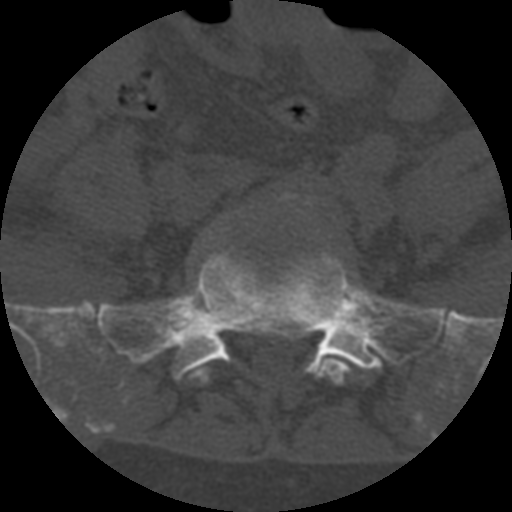
CT including the spine, one axial slice. Slice 173 of 708 in the series (ordered by position). Reconstruction kernel STANDARD. One of 3 acquisitions stored at this slice position. Bone window (W 1800 / L 400 HU). 1.25 mm slice thickness. 512 × 512 image matrix, field of view 160 × 160 mm. Patient age 55 years. From the clinical record (not read from this slice): primary cancer: colon; vertebrae with lytic lesions (as recorded): T12, L1, L5.
Outlined on this slice (semi-automatic segmentation, software-assisted and operator-edited):
- L5 vertebra: bounding box [x1, y1, x2, y2] px = [190, 232, 365, 384]